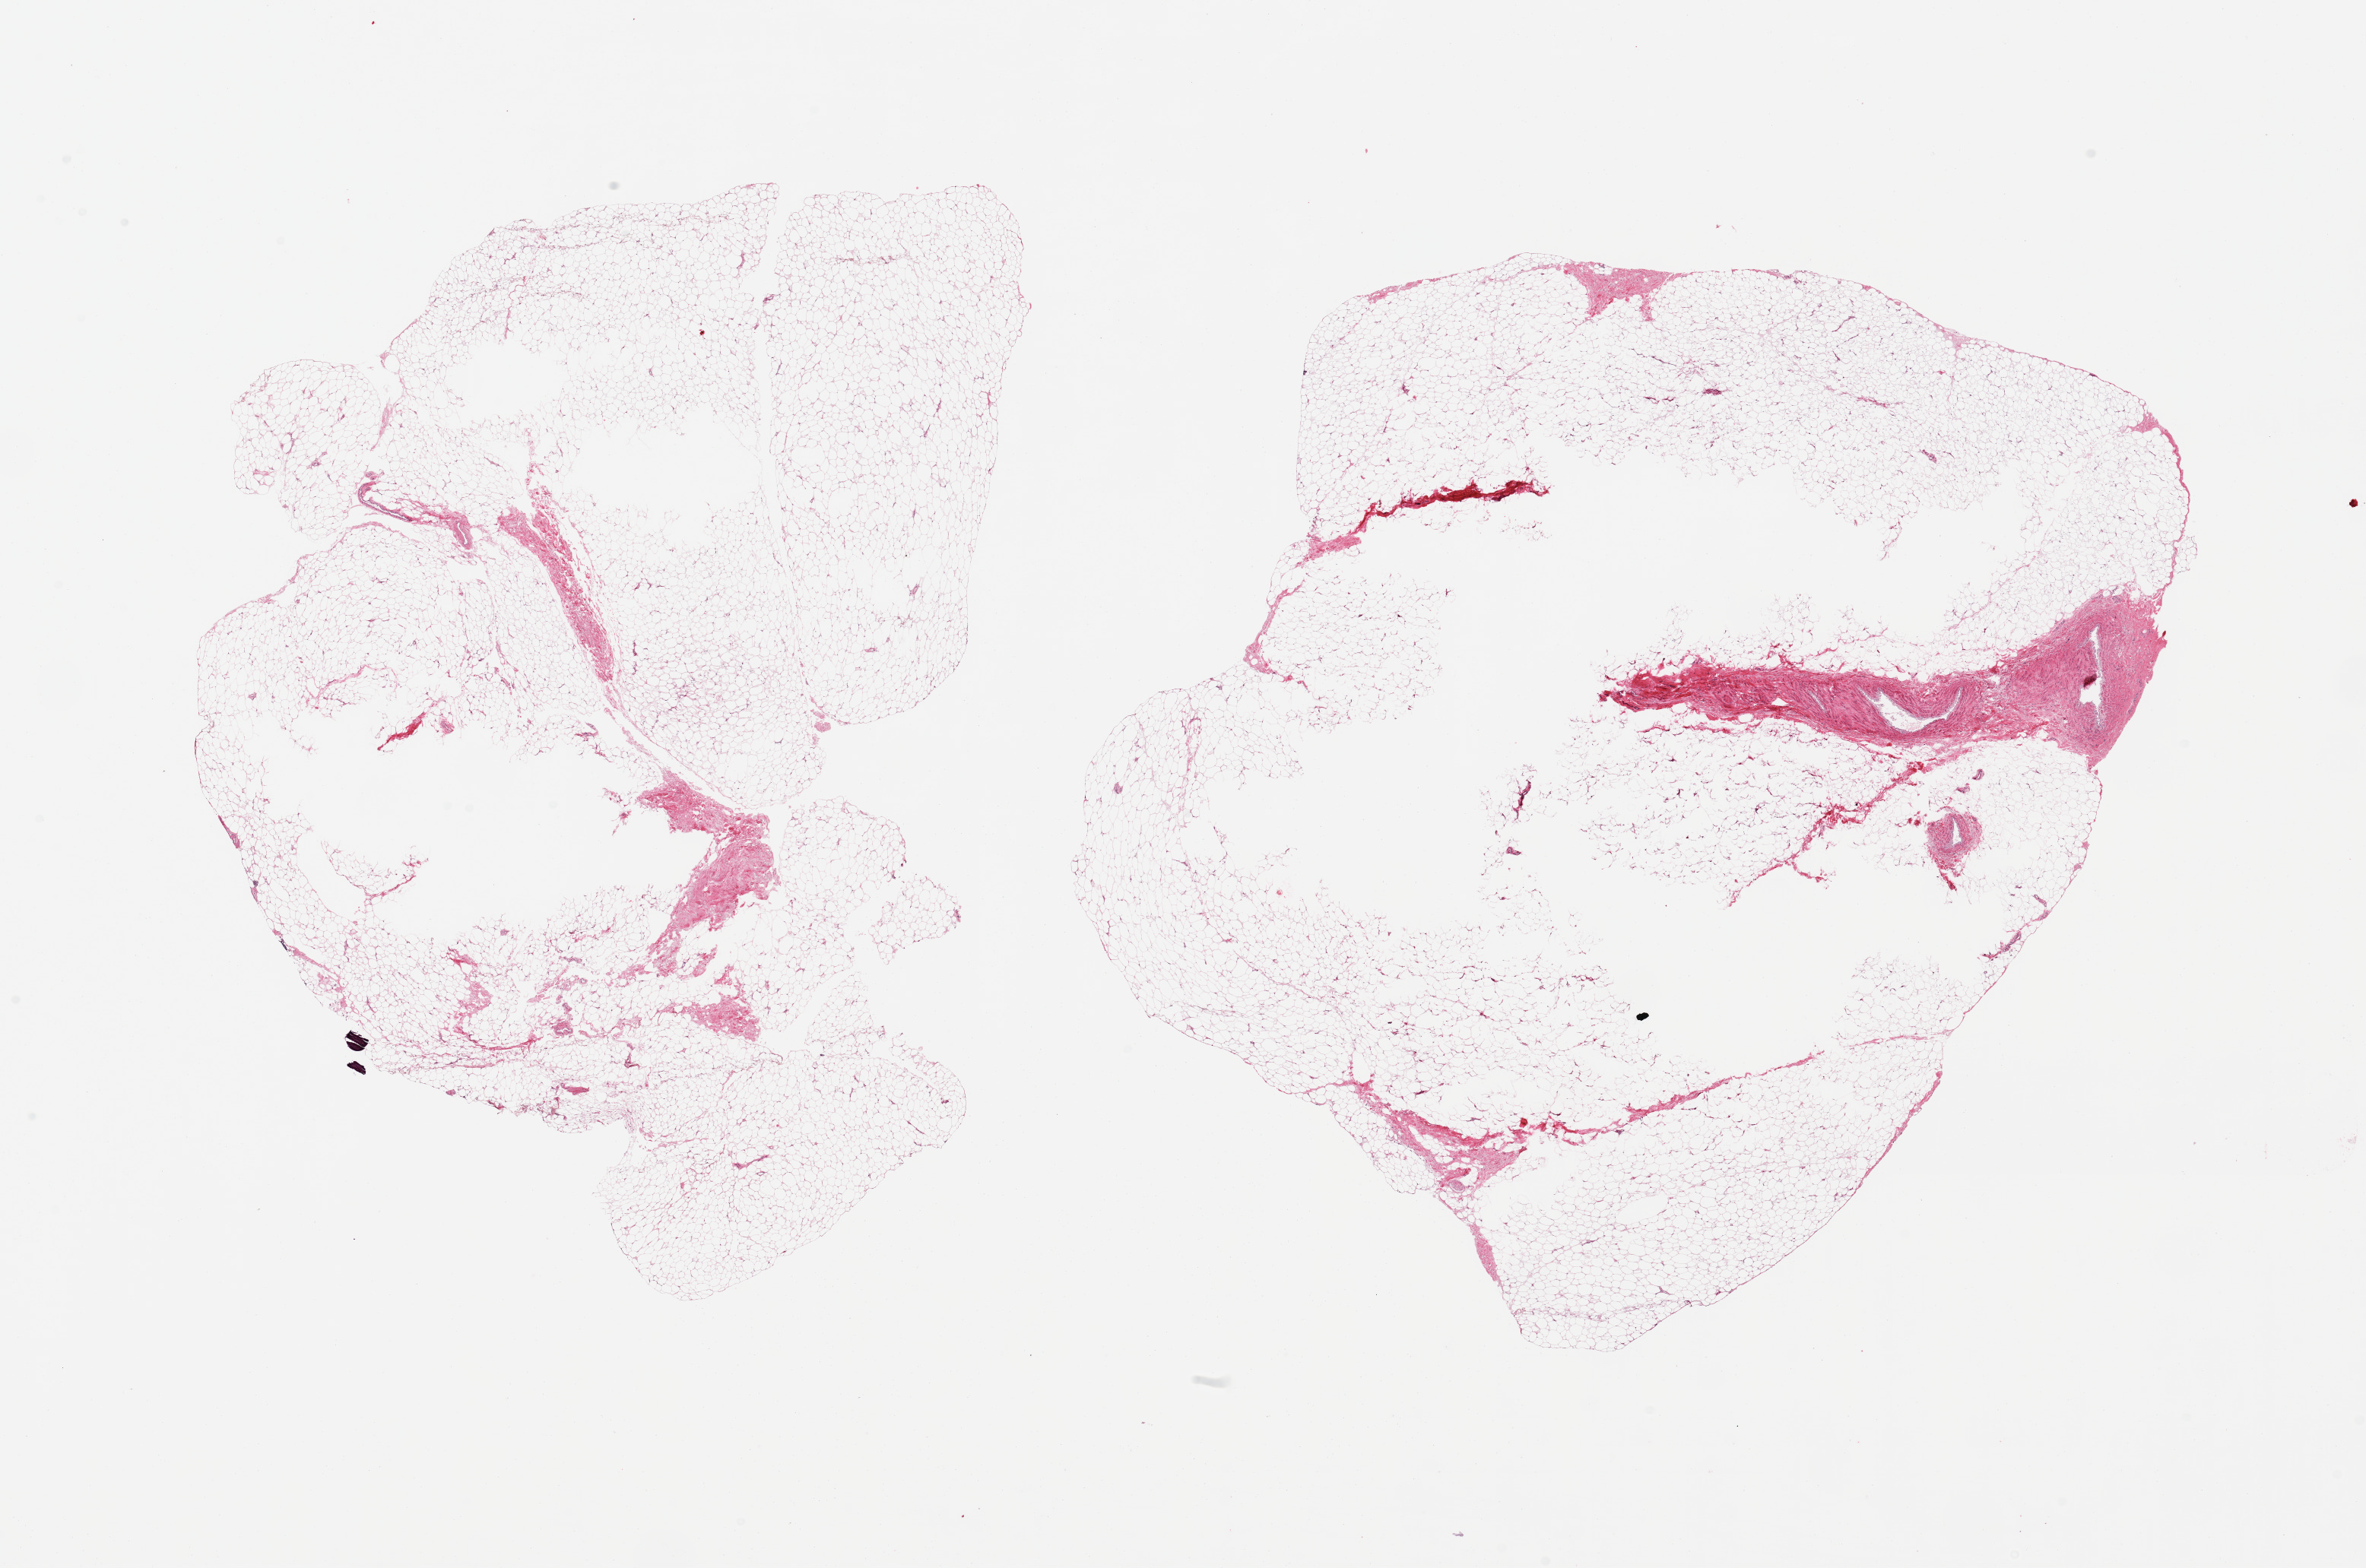
Hematoxylin and eosin (H&E) whole-slide image, a low-resolution overview of the entire scanned area, about 24.6 x 16.3 mm (slide scanned at 20x), PAXgene-fixed paraffin-embedded (PFPE) section, target tissue: breast, tissue donor sample. Male donor.
- reviewer comment on this tissue sample: 2 pieces, fibroadipose elements only